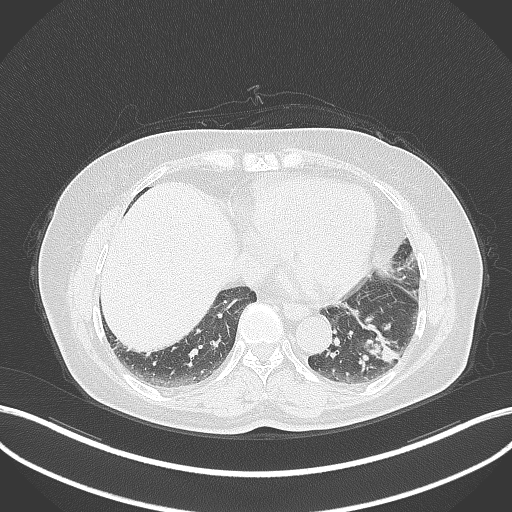
Chest CT, one axial slice; position 119 of 311 along the scan axis; reconstruction kernel B70f; 120 kVp; lung window (W 1500 / L -600 HU); 1 mm slice thickness; 512 × 512 image matrix, field of view 400 × 400 mm. Patient: female, 59 years. From the clinical record (not read from this slice): clinical TNM (as recorded): T2a N0 M0; histopathological grade: G2-3.
Outlined on this slice (rectangle marked by the reading radiologist):
- lung tumour (recorded histology: adenocarcinoma): bounding box [x1, y1, x2, y2] px = [359, 323, 405, 365]